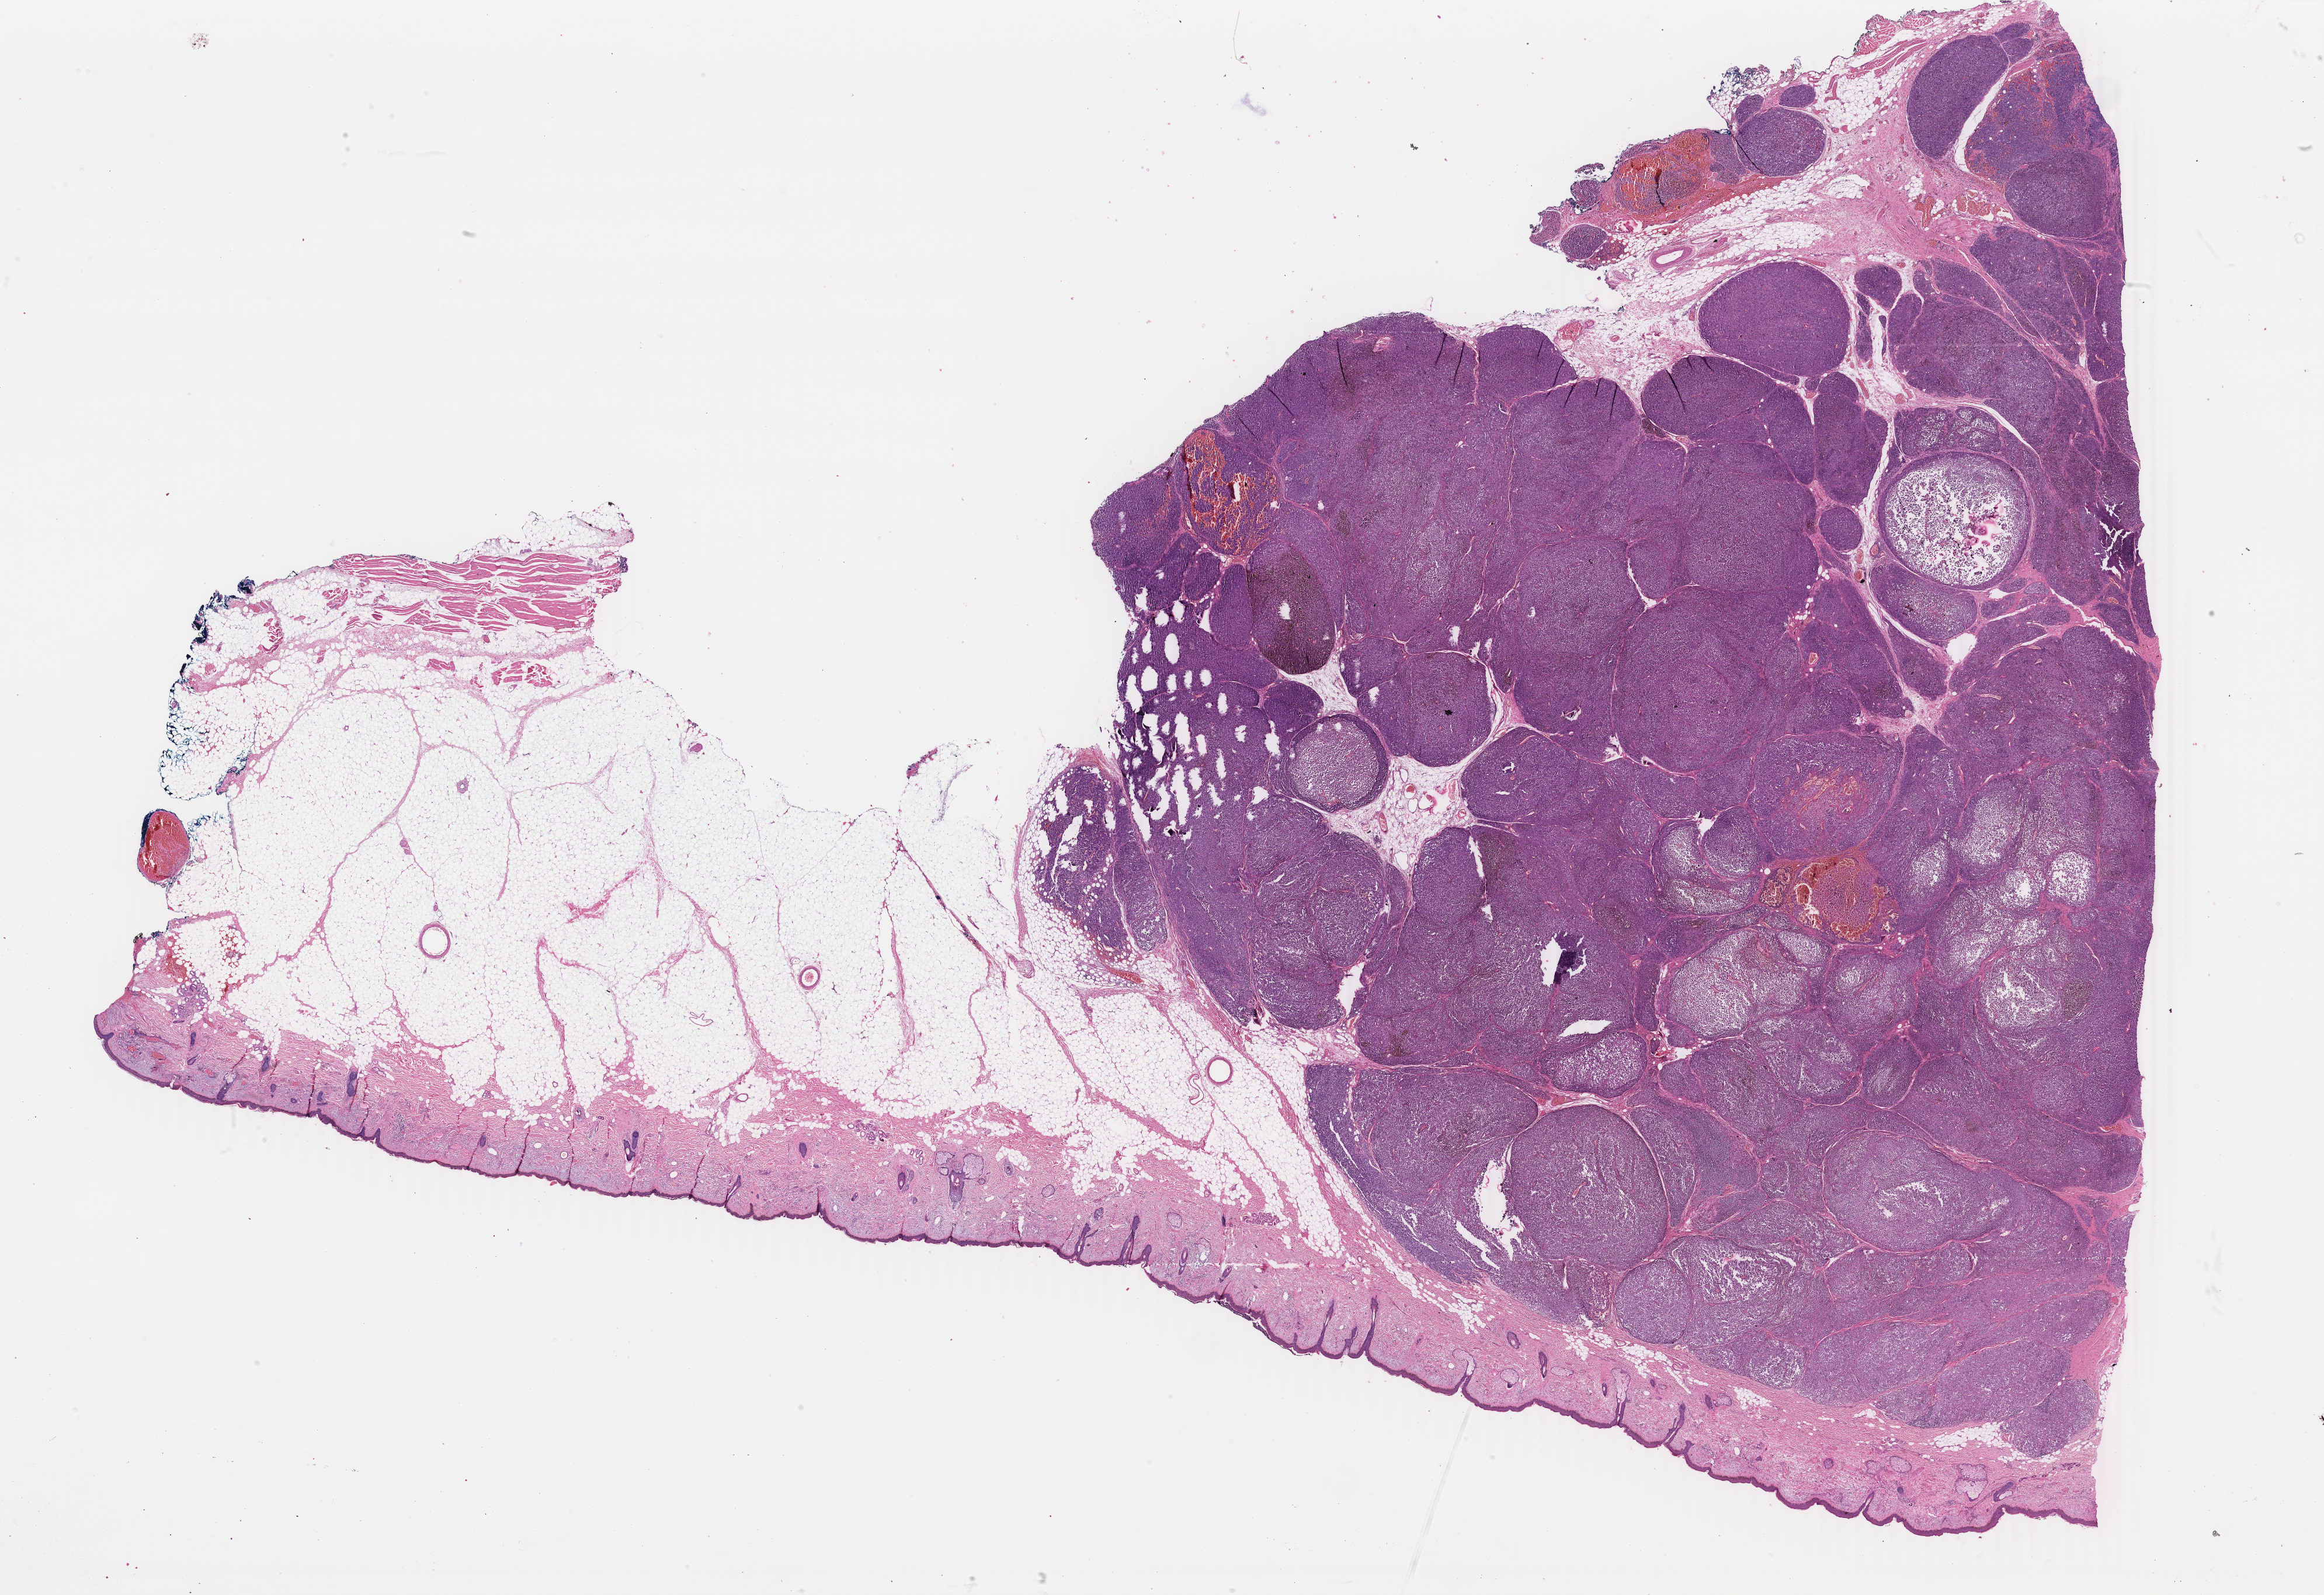
Whole-slide histology image, Hematoxylin and eosin (H&E) stained, whole scanned area (about 31.6 x 21.7 mm, slide scanned at 40x) shown as a low-resolution overview. Formalin-fixed paraffin-embedded (FFPE) diagnostic section. Metastatic tumour sample, sampled site not recorded. Female, age 48 years at initial diagnosis.
* this section: metastatic tumour tissue
* patient diagnosis: Malignant melanoma, NOS